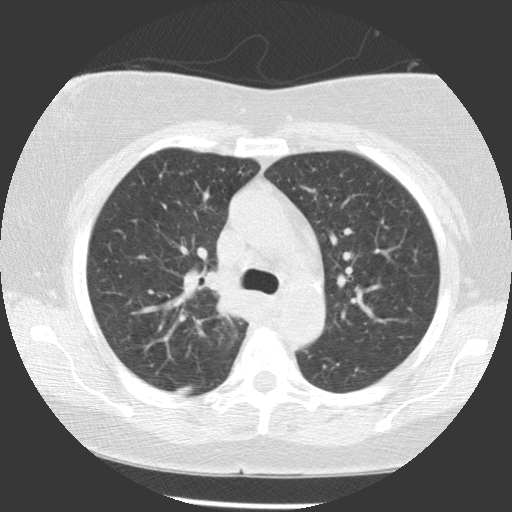
Chest CT (low-dose screening protocol), one axial image. Baseline annual screen. Lung window (W 1500 / L -600 HU). Standard (soft-tissue) reconstruction kernel (STANDARD). Female participant, aged 63 years at enrolment.
Expert-annotated lung lesion, bounding box (x1, y1, x2, y2) in pixels: (186, 262, 250, 323). Reader record for this screening exam (exam-level; its link to the box is not recorded): non-calcified nodule or mass ≥4 mm, right upper lobe, 39 × 36 mm, spiculated (stellate) margins, soft tissue attenuation. Official screen result: positive, change unspecified: nodule(s) >= 4 mm or enlarging nodule(s), mass(es), or other non-specific abnormalities suspicious for lung cancer. Later outcome: lung cancer diagnosed 72 days after this screen — non-small cell carcinoma, right upper lobe, carina, right main stem bronchus, poorly differentiated (G3), stage IIIA (AJCC 6th edition), 66 mm at pathology.